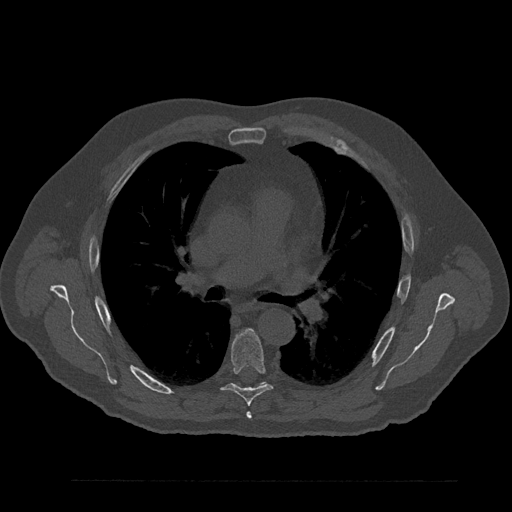
CT including the spine, one axial slice. Slice 554 of 797 in the series (ordered by position). Bone window (W 1800 / L 400 HU). 512 × 512 image matrix, field of view 430 × 430 mm. Male patient, age 61 years. Case-level facts recorded for this patient, not image findings: primary cancer: prostate.
Outlined on this slice (semi-automatic segmentation, software-assisted and operator-edited):
- T5 vertebra: bounding box [x1, y1, x2, y2] px = [246, 412, 252, 419]
- T6 vertebra: [212, 330, 273, 406]
- T7 vertebra: [238, 382, 266, 385]